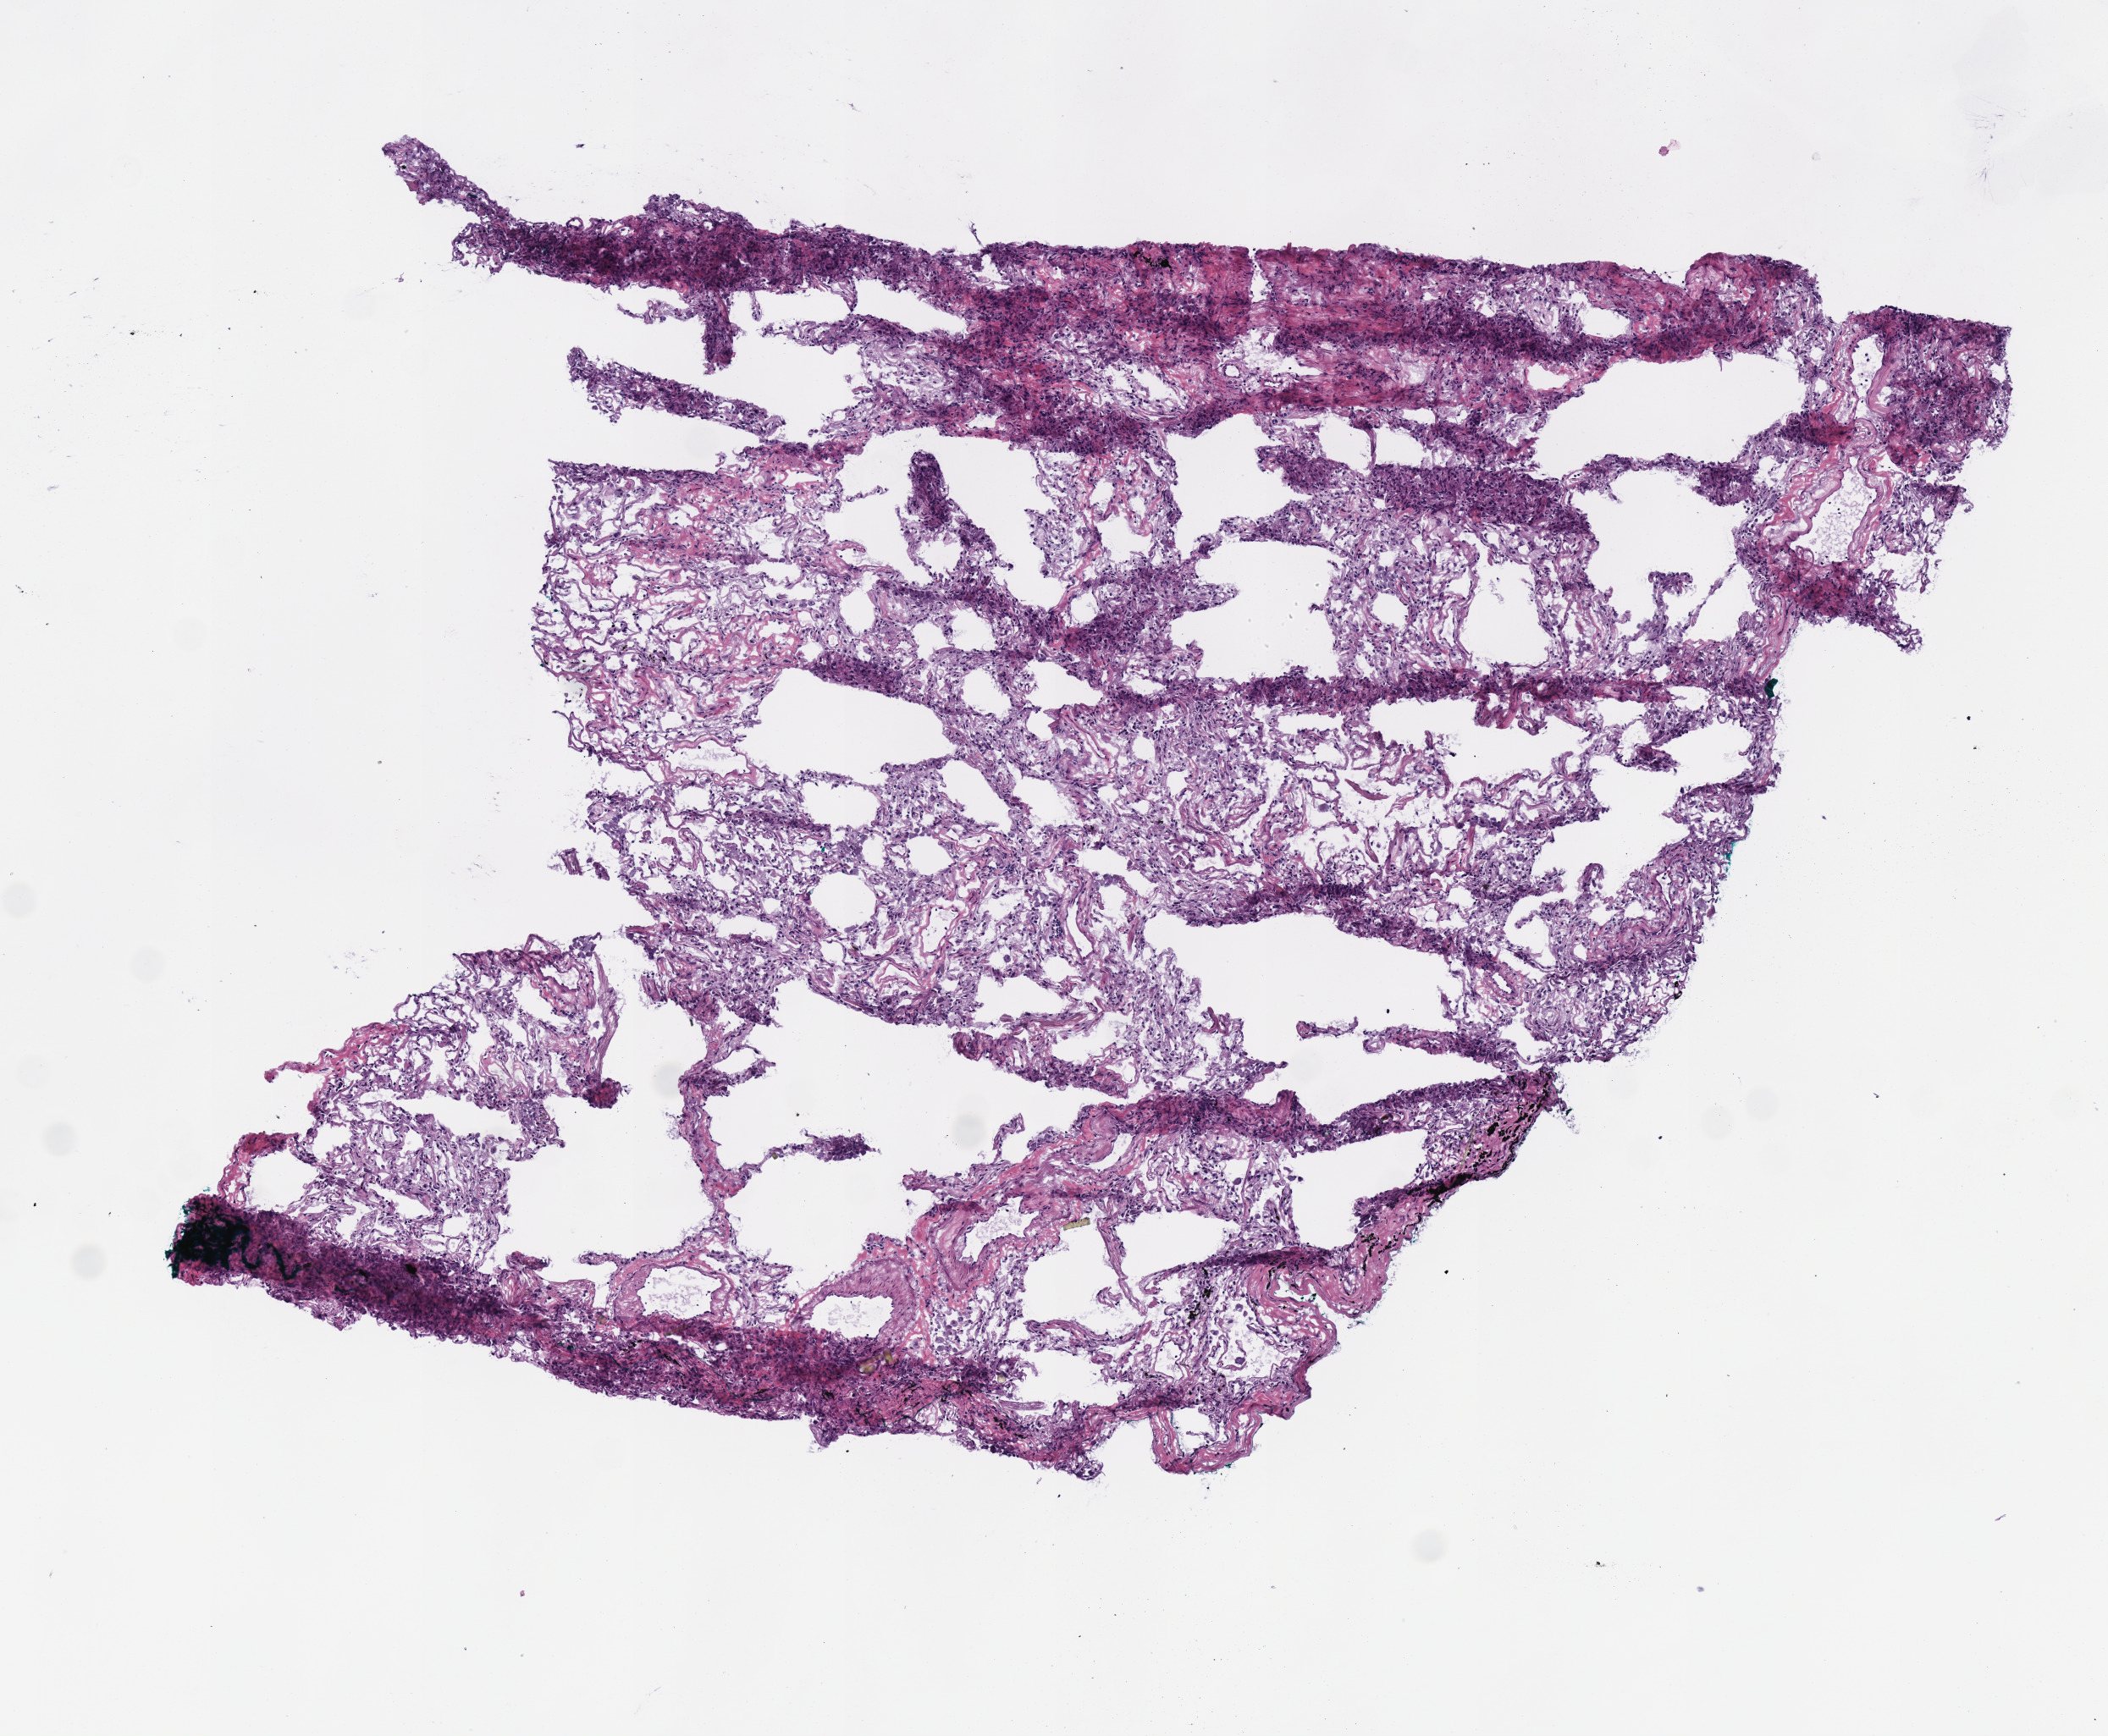
Digitized H&E-stained tissue section (whole slide) — a low-resolution overview of the entire scanned area, about 4.9 x 4.0 mm, frozen section from the top of the tissue portion, solid tissue normal (non-tumour tissue) sample from the lung. Patient: female, age at initial diagnosis 73 years.
• this section: solid tissue normal sample (biorepository sample class)
• patient diagnosis: Adenocarcinoma, NOS (upper lobe, lung)